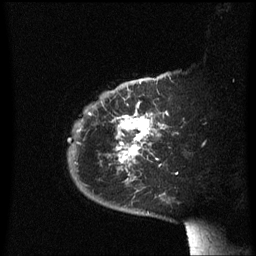
Breast MRI (dynamic contrast-enhanced), one sagittal slice; position 47 of 60 along the scan axis; dynamic contrast-enhanced series, image 2 of 3 at this slice position (ordered by acquisition); 1.5 T; TE 4.2 ms, TR 8.4 ms; 2.3 mm slice thickness; 256 × 256 image matrix, field of view 200 × 200 mm. Patient: female, 38 years. From the clinical record (not read from this slice): setting: breast cancer imaged before/during neoadjuvant chemotherapy; receptor status: HER2-positive.
Structures marked on this image (semi-automatic segmentation, software-assisted and operator-edited):
- analysis volume of interest (the breast-tissue region the enhancement analysis was run in; not a lesion): bounding box <68,78,179,213> (left, top, right, bottom; pixels)
- tumour enhancement mask (voxels above the 70 % enhancement threshold inside the analysis volume of interest): <88,82,168,177>